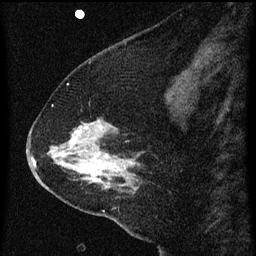
Breast MRI (dynamic contrast-enhanced), one sagittal slice. Slice 21 of 60 in the series (ordered by position). Dynamic contrast-enhanced series, image 2 of 3 at this slice position (ordered by acquisition). 1.5 T. TE 4.2 ms, TR 8 ms. 2 mm slice thickness. 256 × 256 image matrix, field of view 180 × 180 mm. Female patient, age 47 years.
Annotated regions visible in this slice (semi-automatic segmentation, software-assisted and operator-edited):
- analysis volume of interest (the breast-tissue region the enhancement analysis was run in; not a lesion): bounding box <36,106,145,213> (left, top, right, bottom; pixels)
- tumour enhancement mask (voxels above the 70 % enhancement threshold inside the analysis volume of interest): <48,124,130,189>